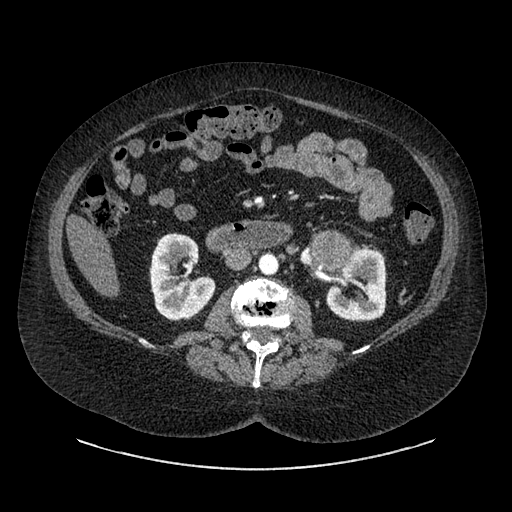
Contrast-enhanced abdominal CT, one axial slice. Slice 490 of 769 in the series (ordered by position). 120 kVp. Intravenous contrast given. Soft-tissue window (W 400 / L 40 HU). 0.62 mm slice thickness. 512 × 512 image matrix, field of view 460 × 460 mm. Female patient, age 61 years. Case-level facts recorded for this patient, not image findings: diagnosis: adrenocortical carcinoma; tumour side: left adrenal; tumour size at pathology: 13 cm; Ki-67 index: 79 %; stage (as recorded): 2.
Annotated regions visible in this slice (semi-automatic segmentation, software-assisted and operator-edited):
- mass: box from (x=317, y=237) to (x=348, y=267) px